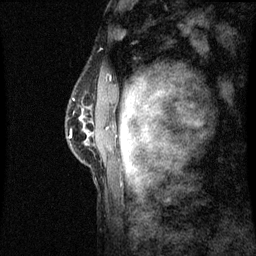
Breast MRI (dynamic contrast-enhanced), one sagittal slice. Position 48 of 60 along the scan axis. Dynamic contrast-enhanced series, image 2 of 3 at this slice position (ordered by acquisition). 1.5 T. TE 4.2 ms, TR 8.9 ms. 256 × 256 image matrix, field of view 200 × 200 mm. Female patient, age 50 years. Case-level facts recorded for this patient, not image findings: setting: breast cancer imaged before/during neoadjuvant chemotherapy; receptor status: triple-negative.
Structures marked on this image (semi-automatic segmentation, software-assisted and operator-edited):
- analysis volume of interest (the breast-tissue region the enhancement analysis was run in; not a lesion): bounding box [x1, y1, x2, y2] px = [68, 86, 97, 167]
- tumour enhancement mask (voxels above the 70 % enhancement threshold inside the analysis volume of interest): [71, 132, 89, 137]